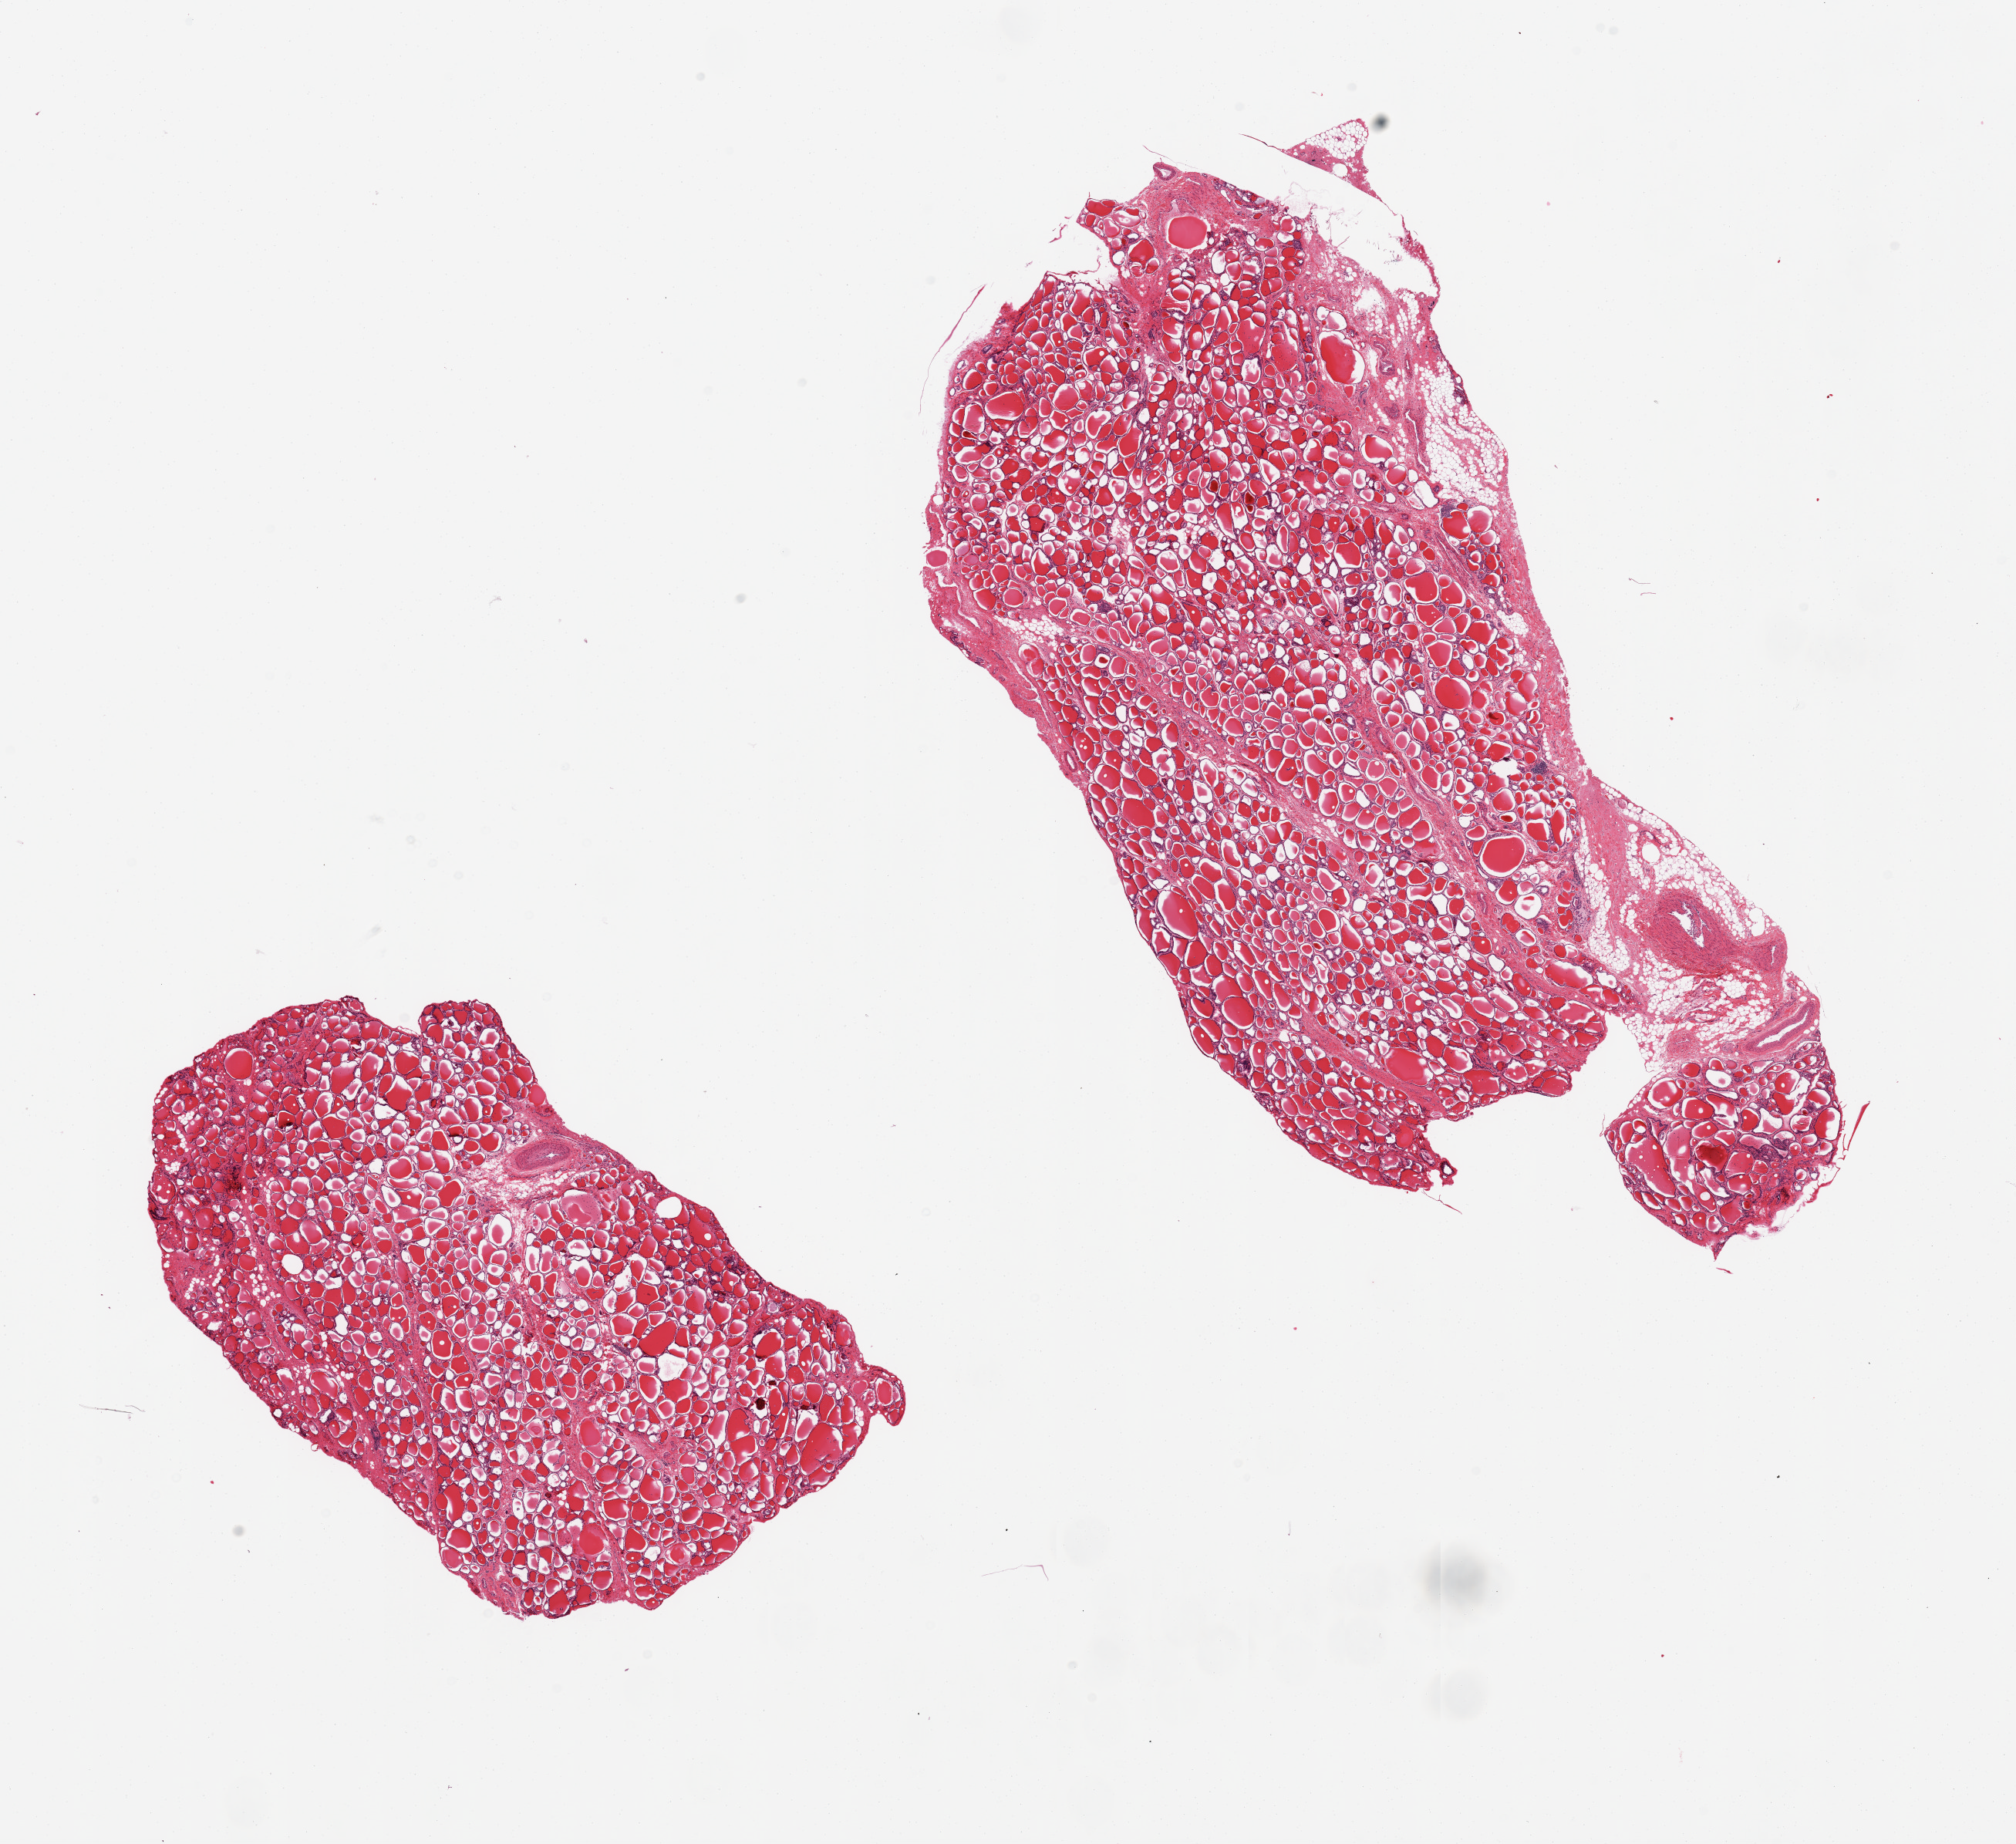
Digitized H&E-stained section, brightfield, shown as a low-resolution overview of the whole scanned area (about 20.7 x 18.9 mm); PAXgene-fixed, paraffin-embedded tissue; target tissue: thyroid; donor tissue sample. Female donor.
Reviewer comment on this tissue sample: 2 pieces, few small lymphoid aggregates, not sufficient for Hashimotos, but may be early stage condition.